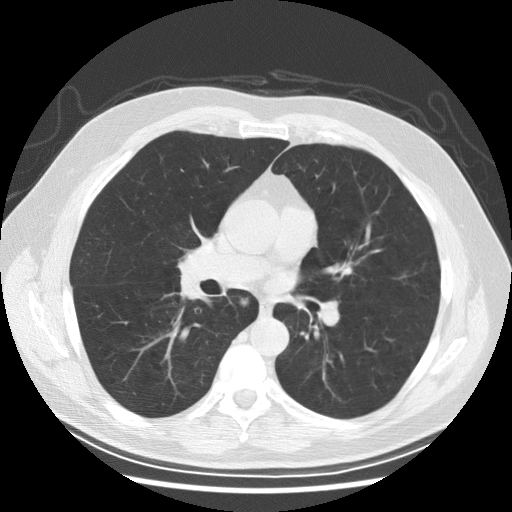
Chest CT (low-dose screening protocol), one axial image; second annual screen; lung window (W 1500 / L -600 HU); 120 kVp; slice 113 of 246 in the series; 512 × 512 image matrix, field of view 370 × 370 mm. Male participant, aged 61 years at enrolment. Former smoker at enrolment.
Lesion marked by an expert reader, bounding box <224,285,257,317> (left, top, right, bottom; pixels). Screening reader's record for this exam: no non-calcified nodule ≥4 mm recorded. Official screen result: negative screen, minor abnormalities not suspicious for lung cancer. Participant outcome: lung cancer diagnosed 382 days after this screen (after the third annual screen) — squamous cell carcinoma, keratinizing, NOS, right lower lobe, stage IIIB (AJCC 6th edition), 40 mm at pathology.